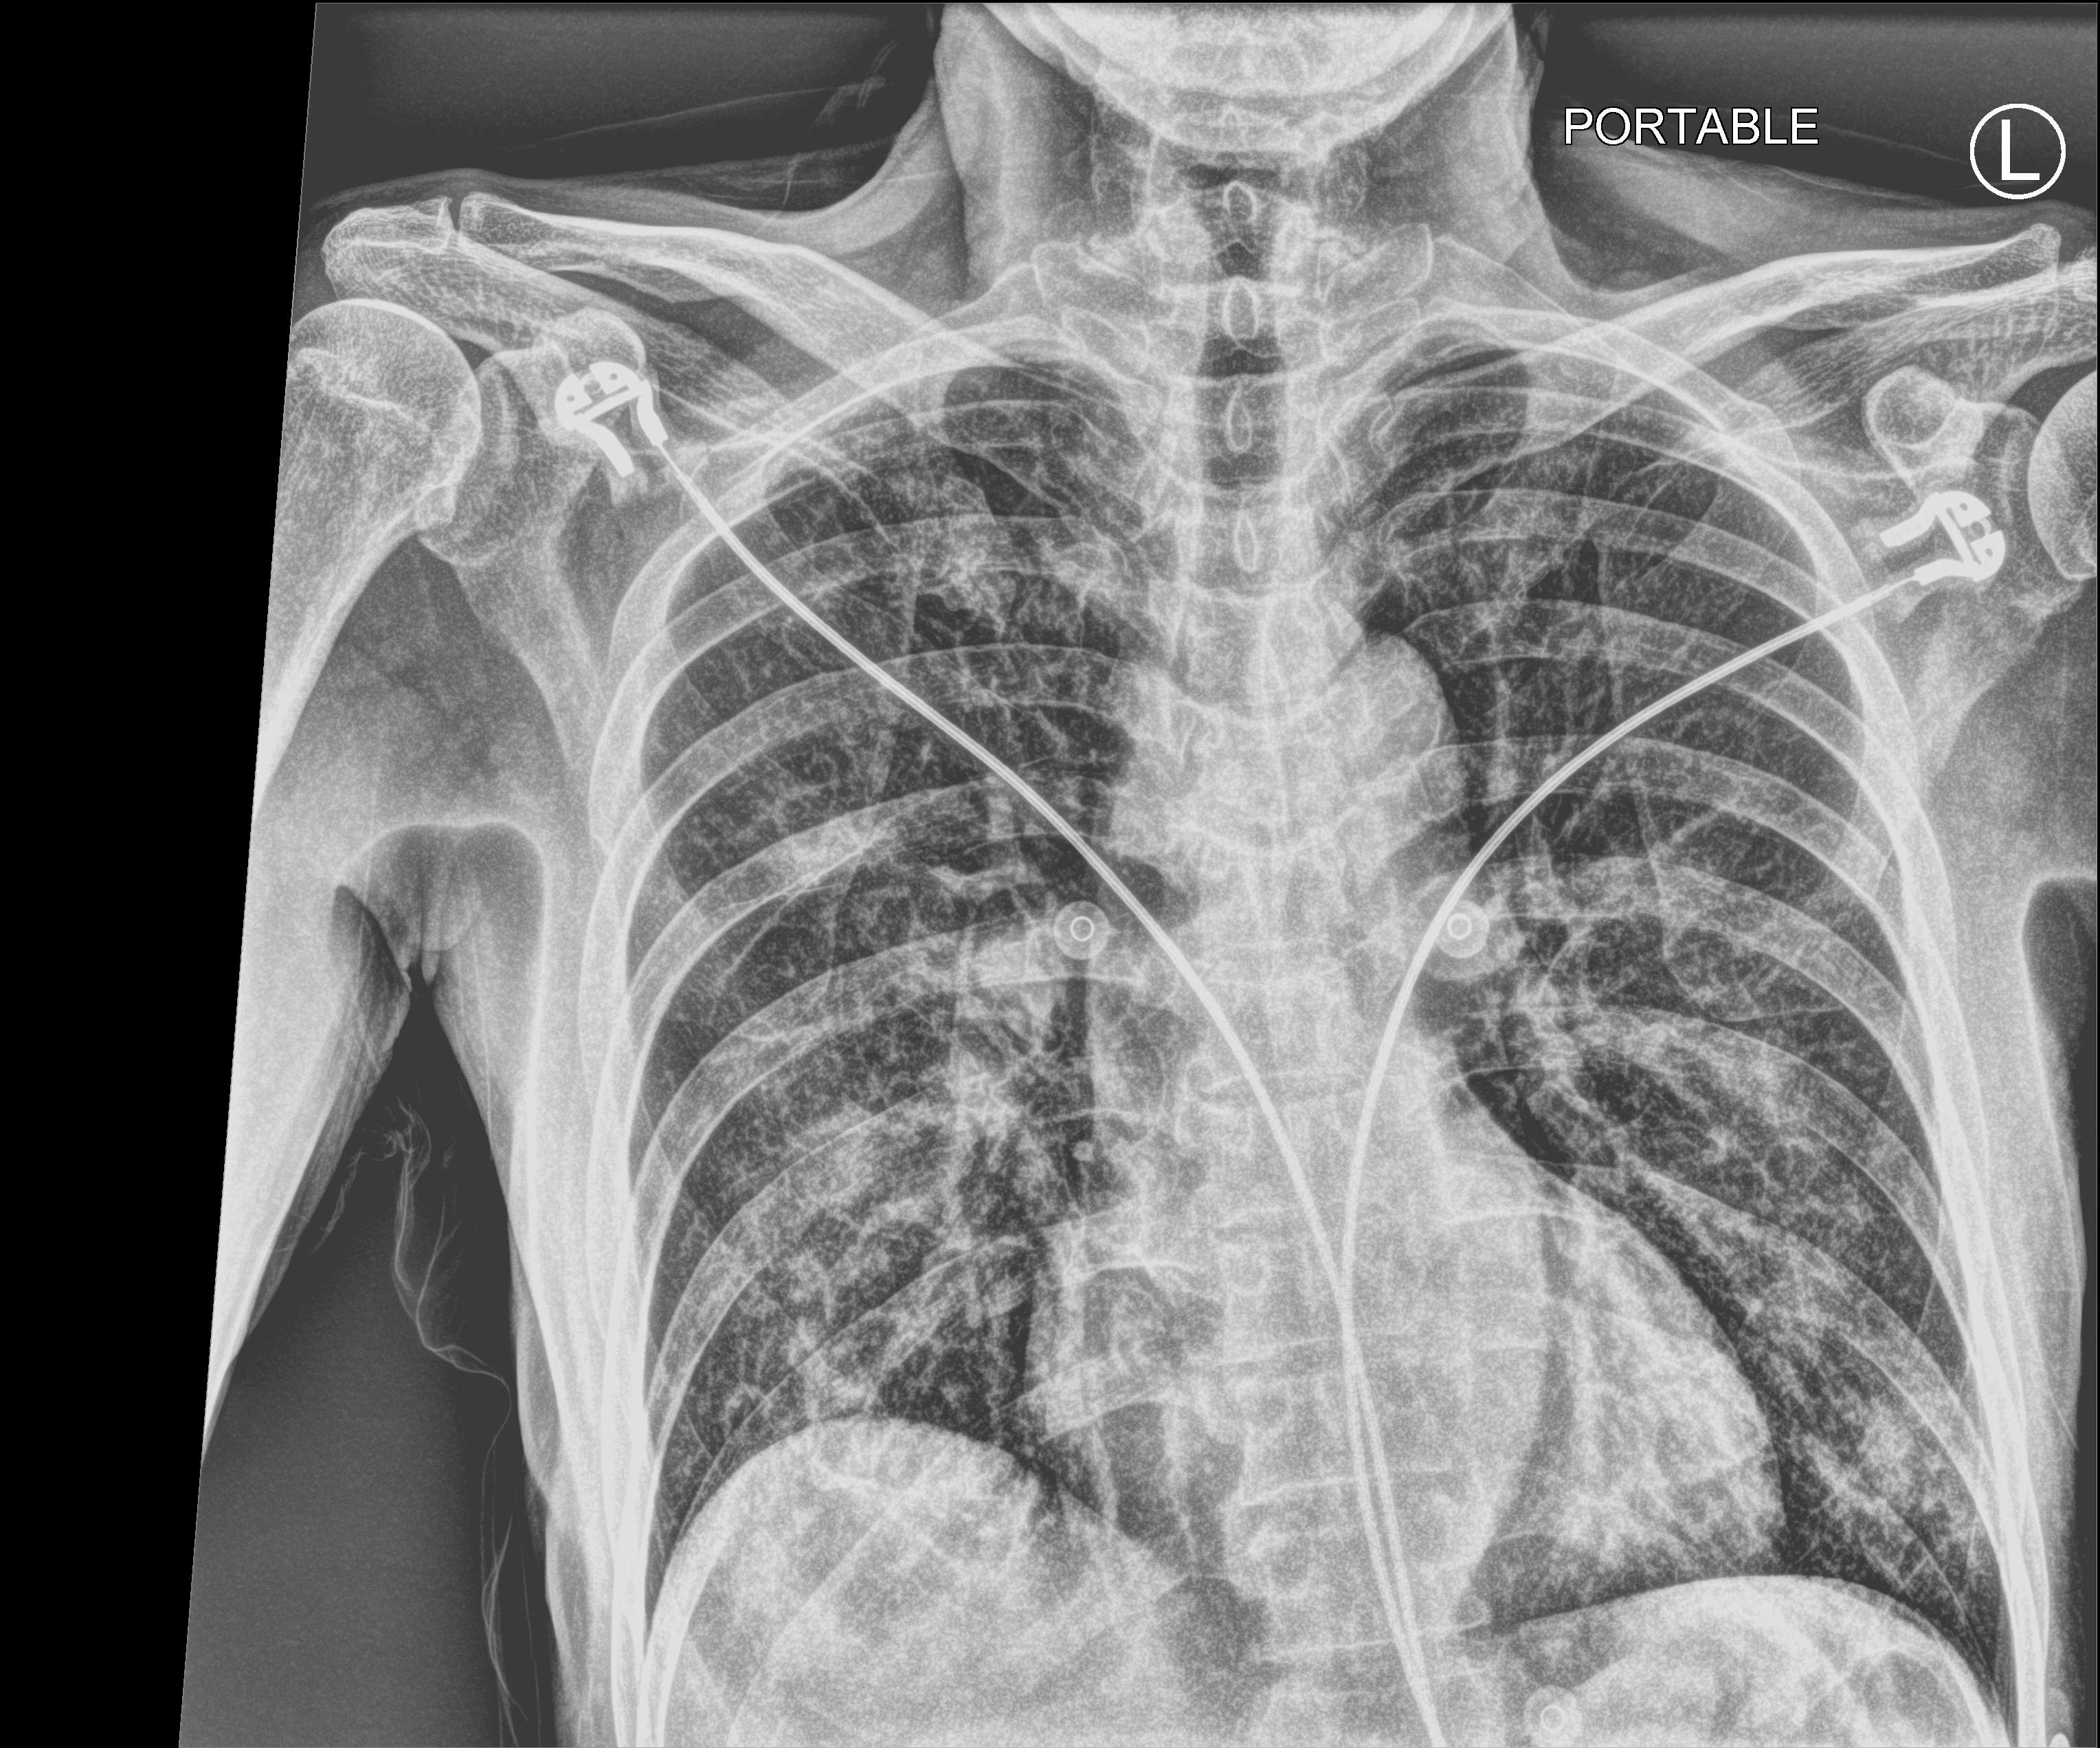
Chest X-ray (portable). Male patient hospitalised with COVID-19, age 60–74 years.
Hospital-stay facts (about this admission, not read from this image; timing relative to this image not recorded):
- admitted to intensive care during this hospital stay: no
- mechanically ventilated during this hospital stay: no